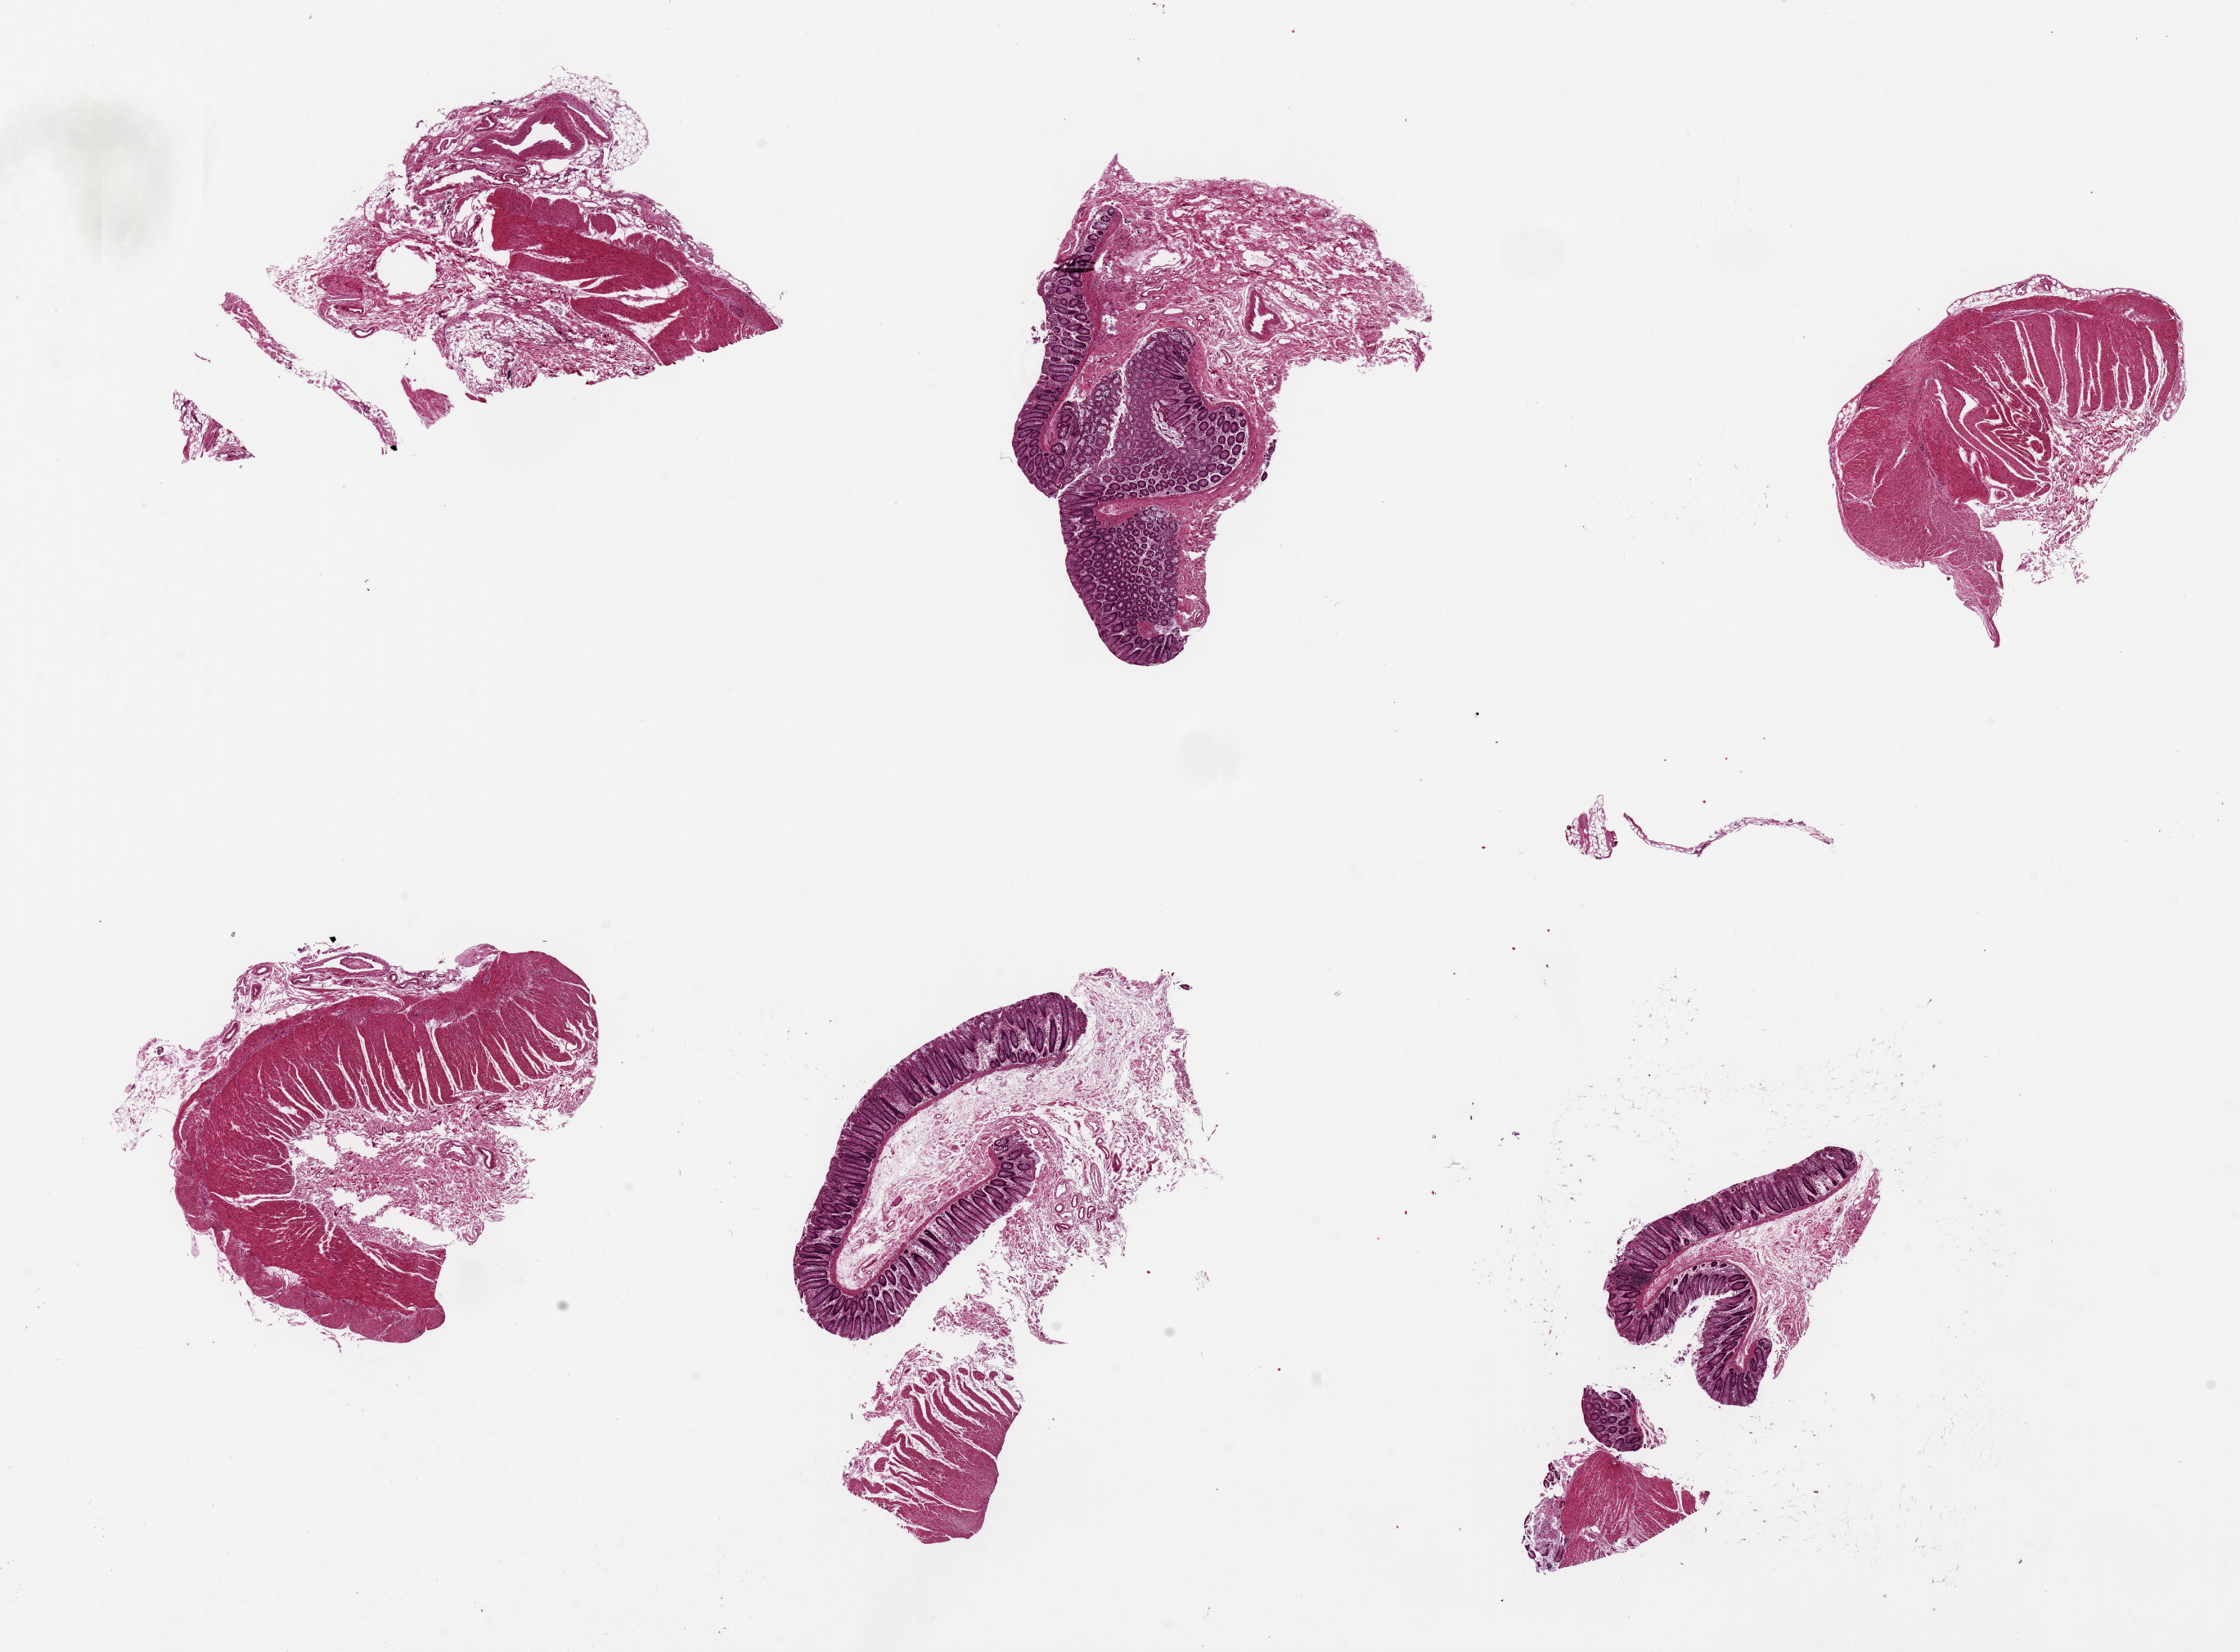
Haematoxylin and eosin whole-slide image, whole scanned area (about 21.7 x 16.0 mm) shown as a low-resolution overview, PAXgene-fixed paraffin-embedded (PFPE) section, section of transverse colon (target tissue), tissue donor sample. Male donor.
- review note (as recorded): 6 pieces up to 6x3 mm; 3 have mucosa without muscularis, 3 have muscularis without mucosa